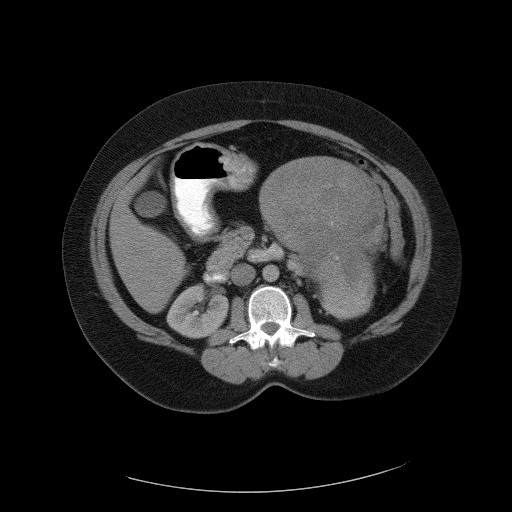
Contrast-enhanced abdominal CT, one axial slice; slice 58 of 90 in the series (ordered by position); 120 kVp; soft-tissue window (W 400 / L 40 HU); 5 mm slice thickness; 512 × 512 image matrix, field of view 480 × 480 mm. Female patient, age 55 years. From the clinical record (not read from this slice): diagnosis: adrenocortical carcinoma; tumour side: left adrenal; tumour size at pathology: 22 cm; Ki-67 index: 10 %; stage (as recorded): 3.
Outlined on this slice (semi-automatically segmented with operator editing):
- mass: bounding box [x1, y1, x2, y2] px = [261, 156, 382, 277]